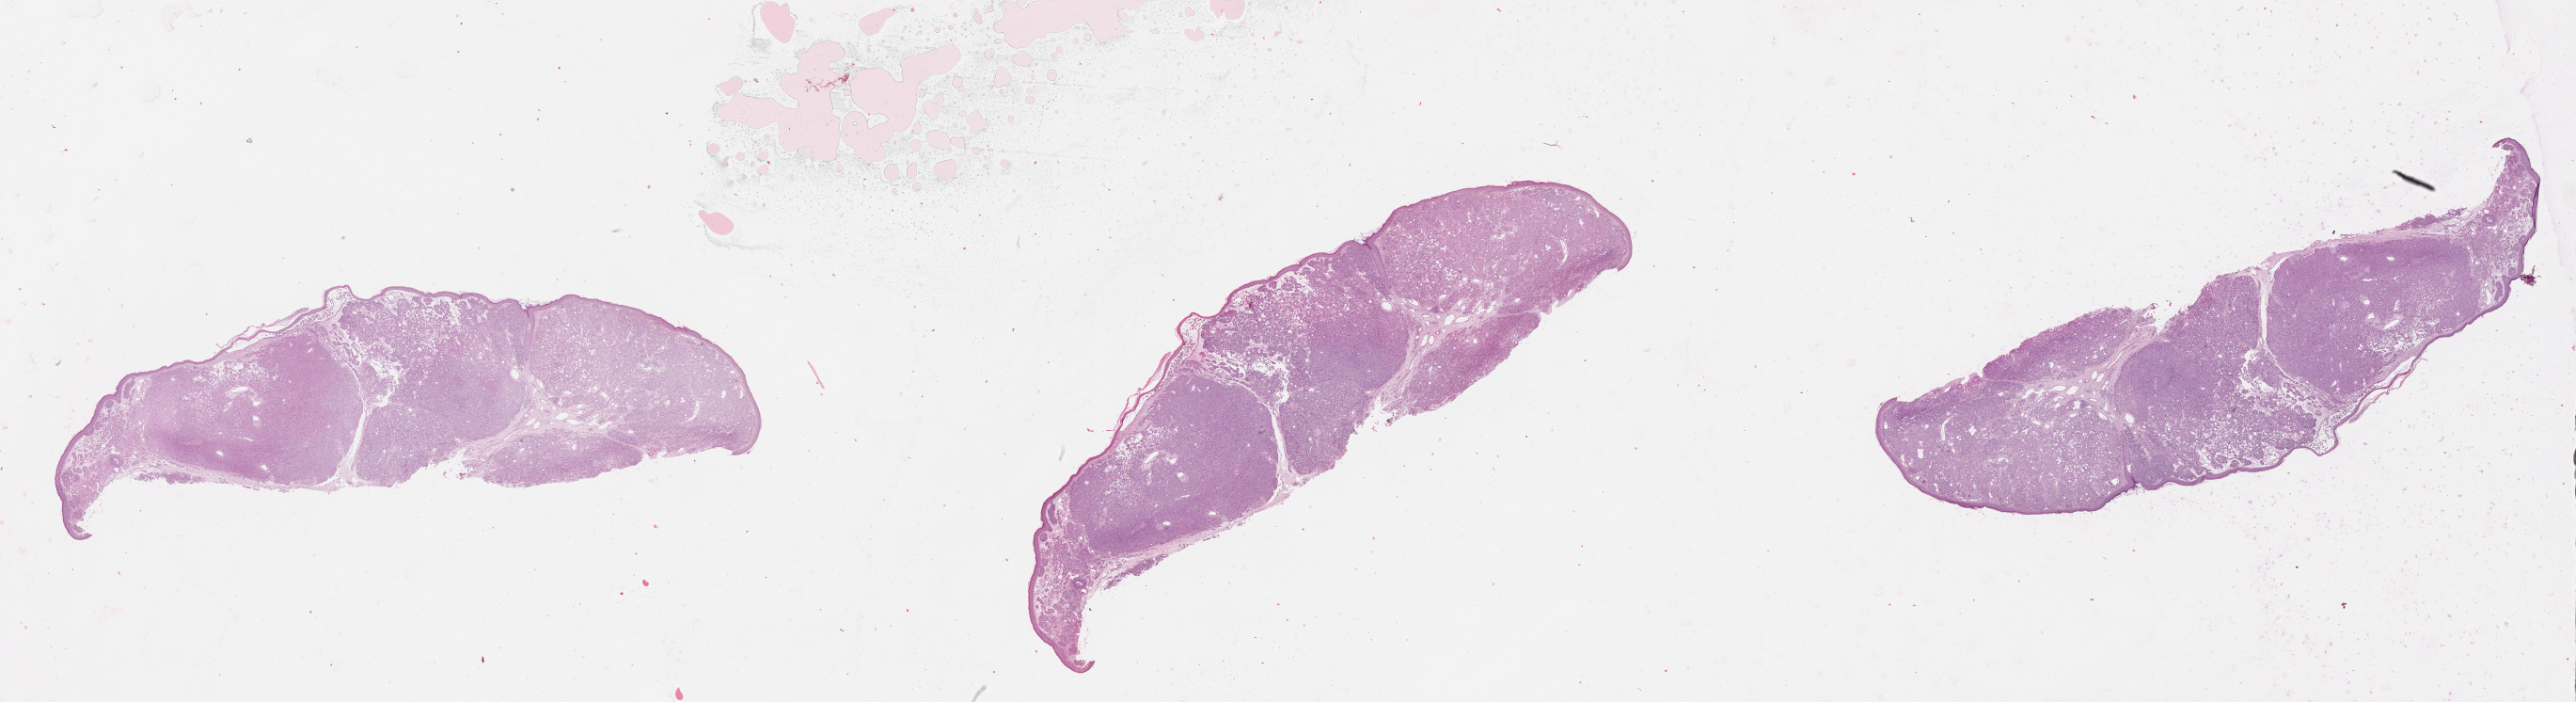
Whole-slide histology image, Hematoxylin and eosin (H&E) stained, whole scanned area (about 44.1 x 12.0 mm, slide scanned at 20x) shown as a low-resolution overview; tumour tissue sample, sampled site: chest. Male, 62 y/o. Pathologist review of this section (percent, as recorded): tumour nuclei 80%, necrosis 0%.
AJCC pathologic stage: IIIC. Histologic diagnosis: Malignant melanoma, NOS.